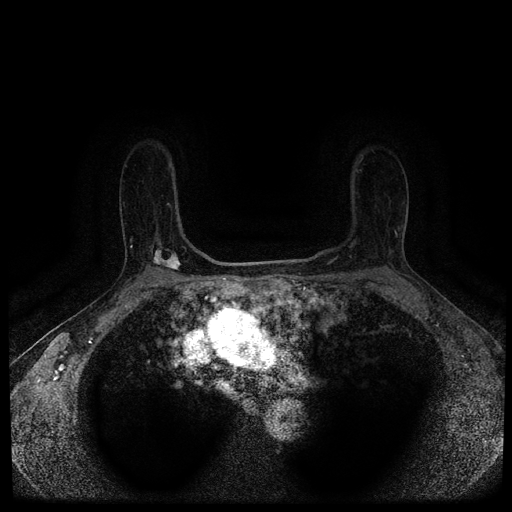
Breast MRI (dynamic contrast-enhanced, multi-phase), one axial slice. Position 74 of 116 along the scan axis. Dynamic contrast-enhanced series, time point 2 of 5 at this slice position (early post-contrast). 1.5 T. TE 2.7 ms, TR 5.4 ms. 2 mm slice thickness. 512 × 512 image matrix, field of view 330 × 330 mm. Female patient, age 63 years.
Structures marked on this image (semi-automatically segmented with operator editing):
- breast lesion (labelled 'tumour' in the annotation; benign lesions carry a separate 'benign' label): box from (x=150, y=249) to (x=182, y=275) px